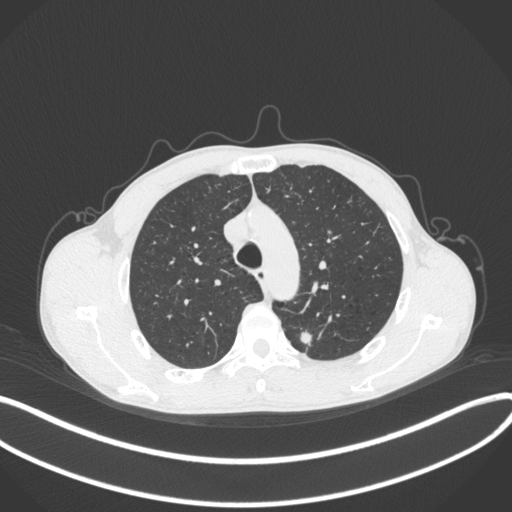
Chest CT, one axial slice; slice 302 of 429 in the series (ordered by position); 120 kVp; lung window (W 1500 / L -600 HU); 1 mm slice thickness; 512 × 512 image matrix. Male patient, age 51 years. From the clinical record (not read from this slice): clinical TNM (as recorded): T2a N1 M1.
Structures marked on this image (bounding box drawn by a radiologist):
- lung tumour (recorded histology: adenocarcinoma): bounding box [x1, y1, x2, y2] px = [299, 328, 315, 349]